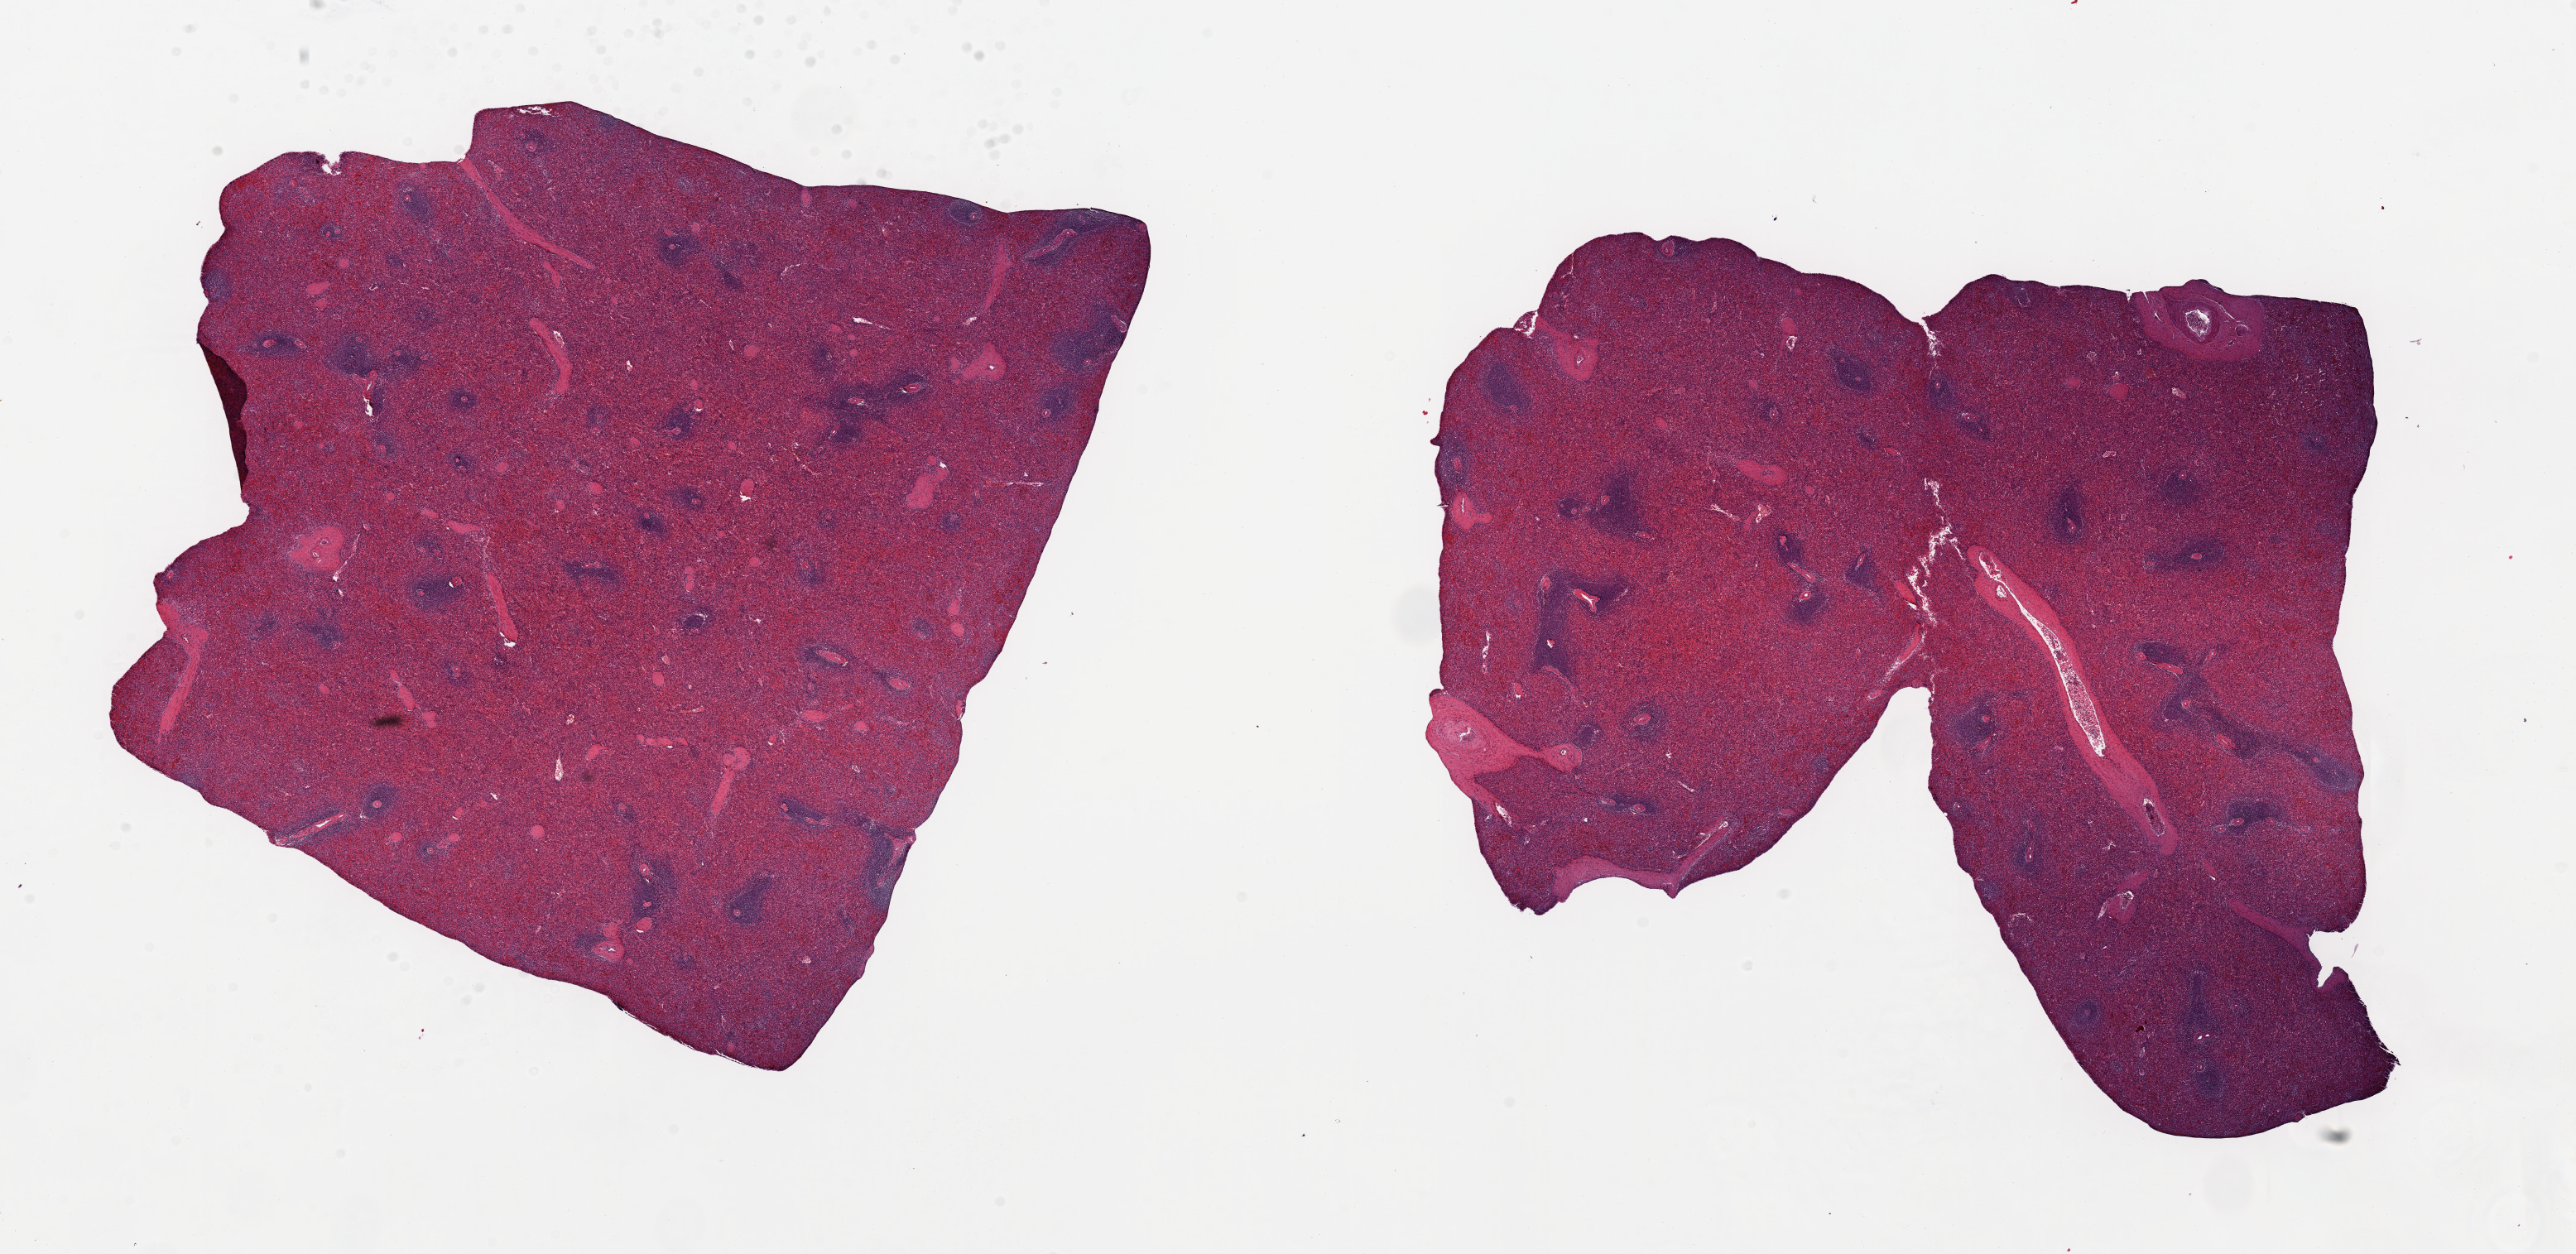
Digitized haematoxylin and eosin-stained section, brightfield, low-resolution overview of the scanned area, about 24.6 x 12.0 mm; PAXgene-fixed, paraffin-embedded tissue; section of spleen (target tissue); donor tissue sample. Donor: female.
Pathologist's review note for this sample: 2 pieces, no abnormalities.